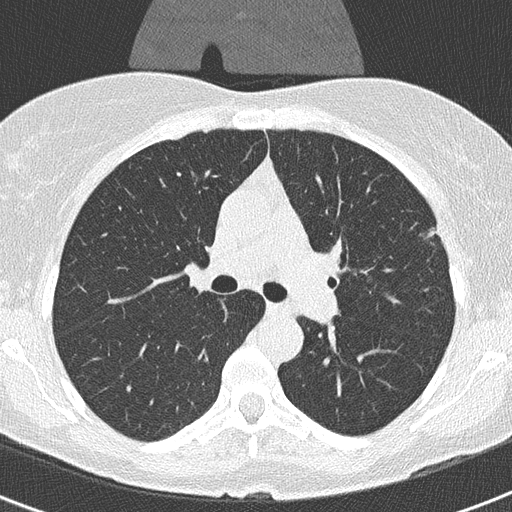
Chest CT (low-dose screening protocol), one axial image. Second screening round (one year after baseline). Lung window (W 1500 / L -600 HU). 2 mm slice thickness. Female participant, aged 56 years at enrolment.
Expert reader's lesion annotation, bounding box <402,201,454,257> (left, top, right, bottom; pixels). Reader record for this screening exam (exam-level; its link to the box is not recorded): non-calcified nodule or mass ≥4 mm, left upper lobe, 20 × 9 mm, smooth margins, soft tissue attenuation, pre-existing on the prior screen: yes; interval growth: yes. Lung cancer was diagnosed 55 days after this screen: adenocarcinoma, NOS, left upper lobe, moderately differentiated (G2), stage IA (AJCC 6th edition), 11 mm at pathology.